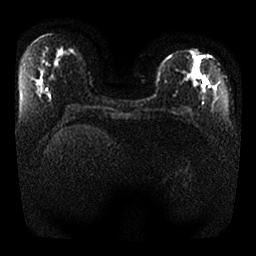
Breast MRI, one axial slice; slice 11 of 25 in the series (ordered by position); diffusion-weighted series; image 2 of 4 stored at this slice position (different b-values; order by instance number); 1.5 T; 4 mm slice thickness; 256 × 256 image matrix. Female patient.
Structures marked on this image (expert manual segmentation):
- tumour on diffusion-weighted imaging: bounding box <183,71,198,88> (left, top, right, bottom; pixels)